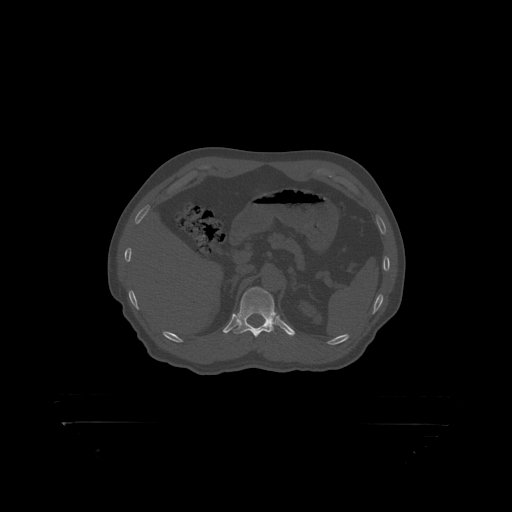
CT including the spine, one axial slice. Slice 353 of 399 in the series (ordered by position). Reconstruction kernel STANDARD. 120 kVp. Bone window (W 1800 / L 400 HU). 512 × 512 image matrix, field of view 650 × 650 mm. Patient: male, 46 years. From the clinical record (not read from this slice): primary cancer: skin.
Outlined on this slice (semi-automatic segmentation, software-assisted and operator-edited):
- T12 vertebra: bounding box [x1, y1, x2, y2] px = [238, 287, 276, 319]